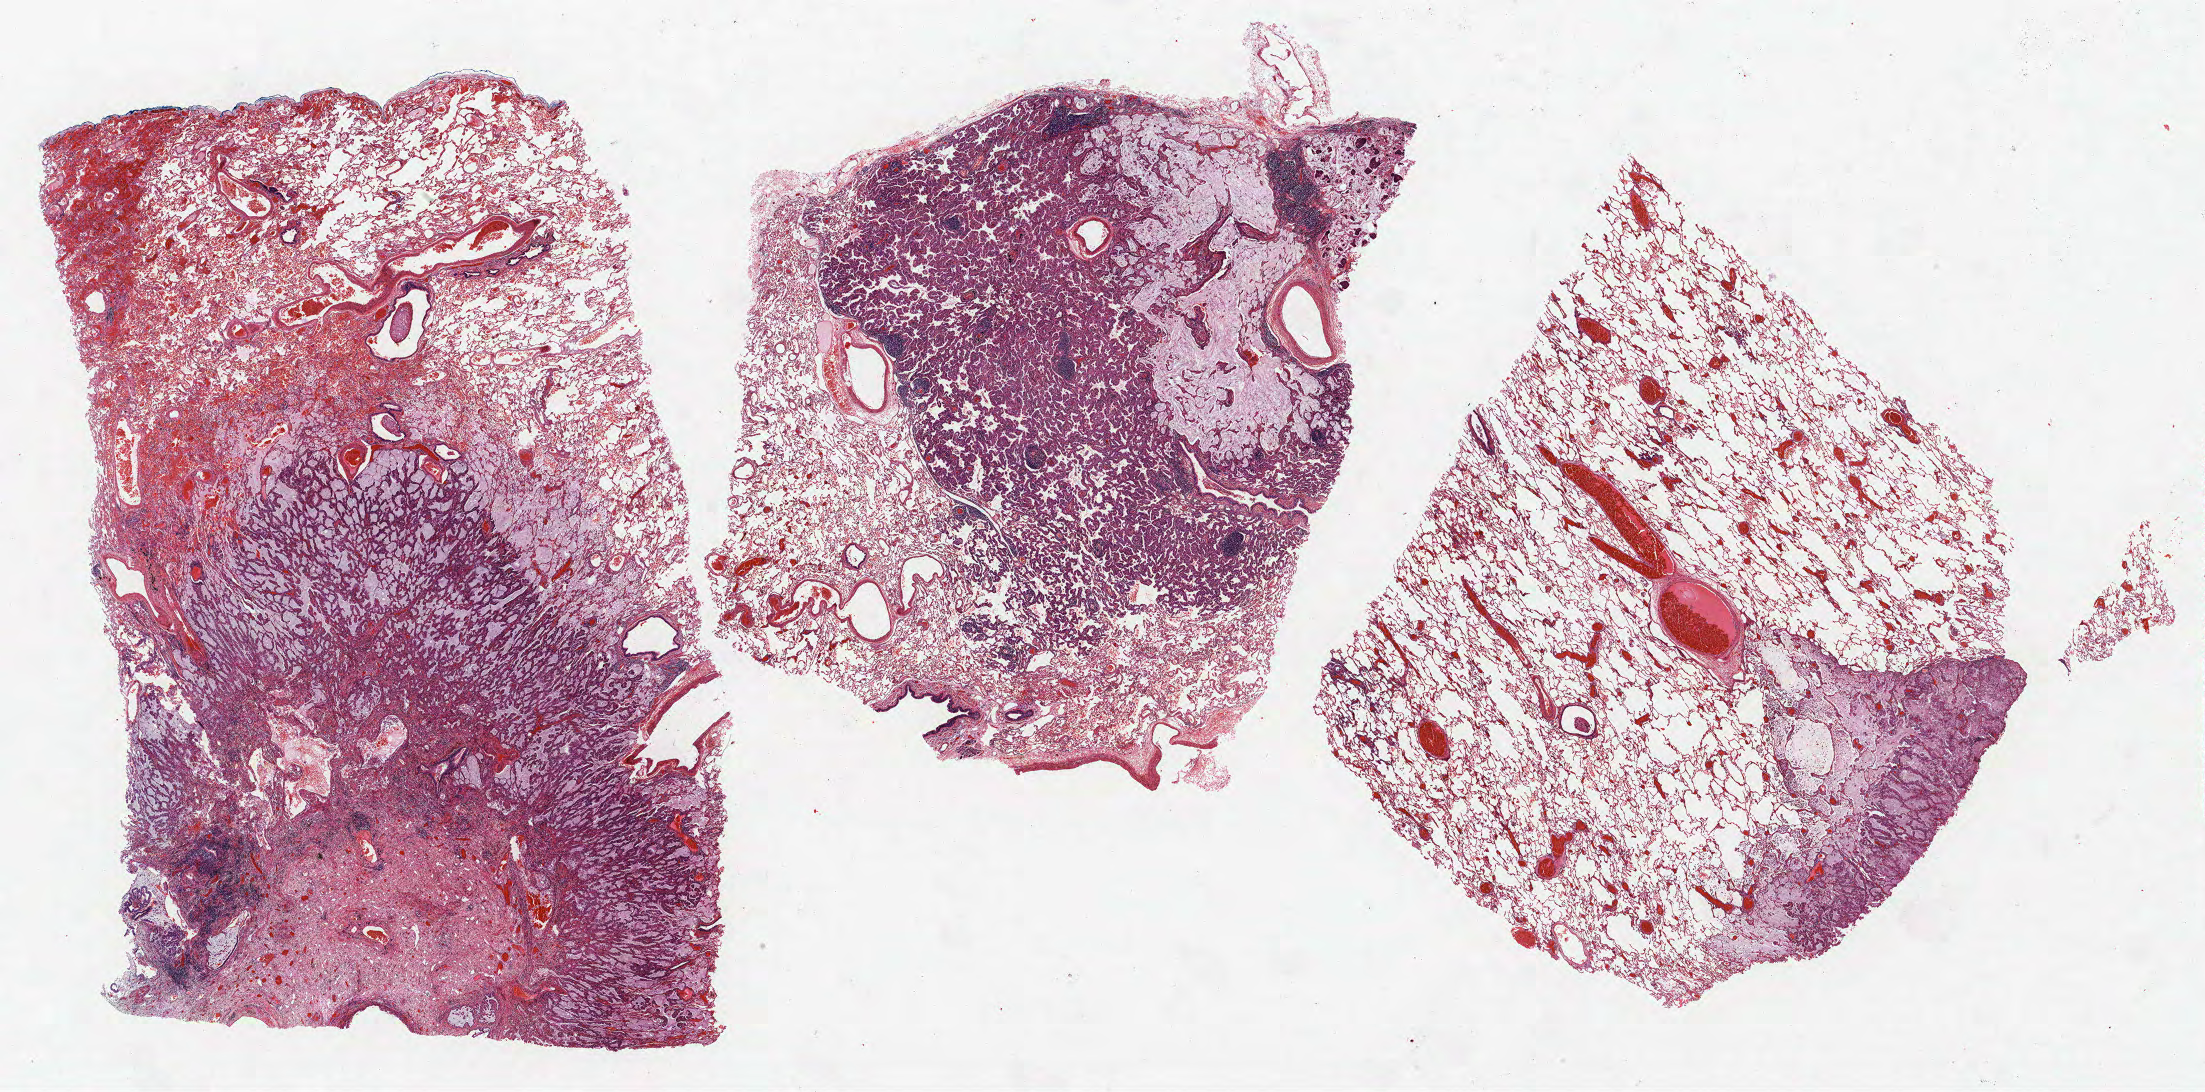
Hematoxylin and eosin (H&E) stained whole-slide image — low-resolution overview of the scanned area, about 35.3 x 17.5 mm, FFPE section, lung. Female patient, aged 61 at enrolment. Current smoker at enrolment. Grade: moderately differentiated (G2).
* ICD-O-3 topography: lower lobe of lung (C34.3)
* participant's lung-cancer diagnosis: Adenocarcinoma, NOS
* primary tumour location (clinical record): right lower lobe
* tumour size (pathology): 30 mm
* stage (AJCC 6th edition): IIA
* note: participant had 2 primary lung cancers recorded; fields above describe the first